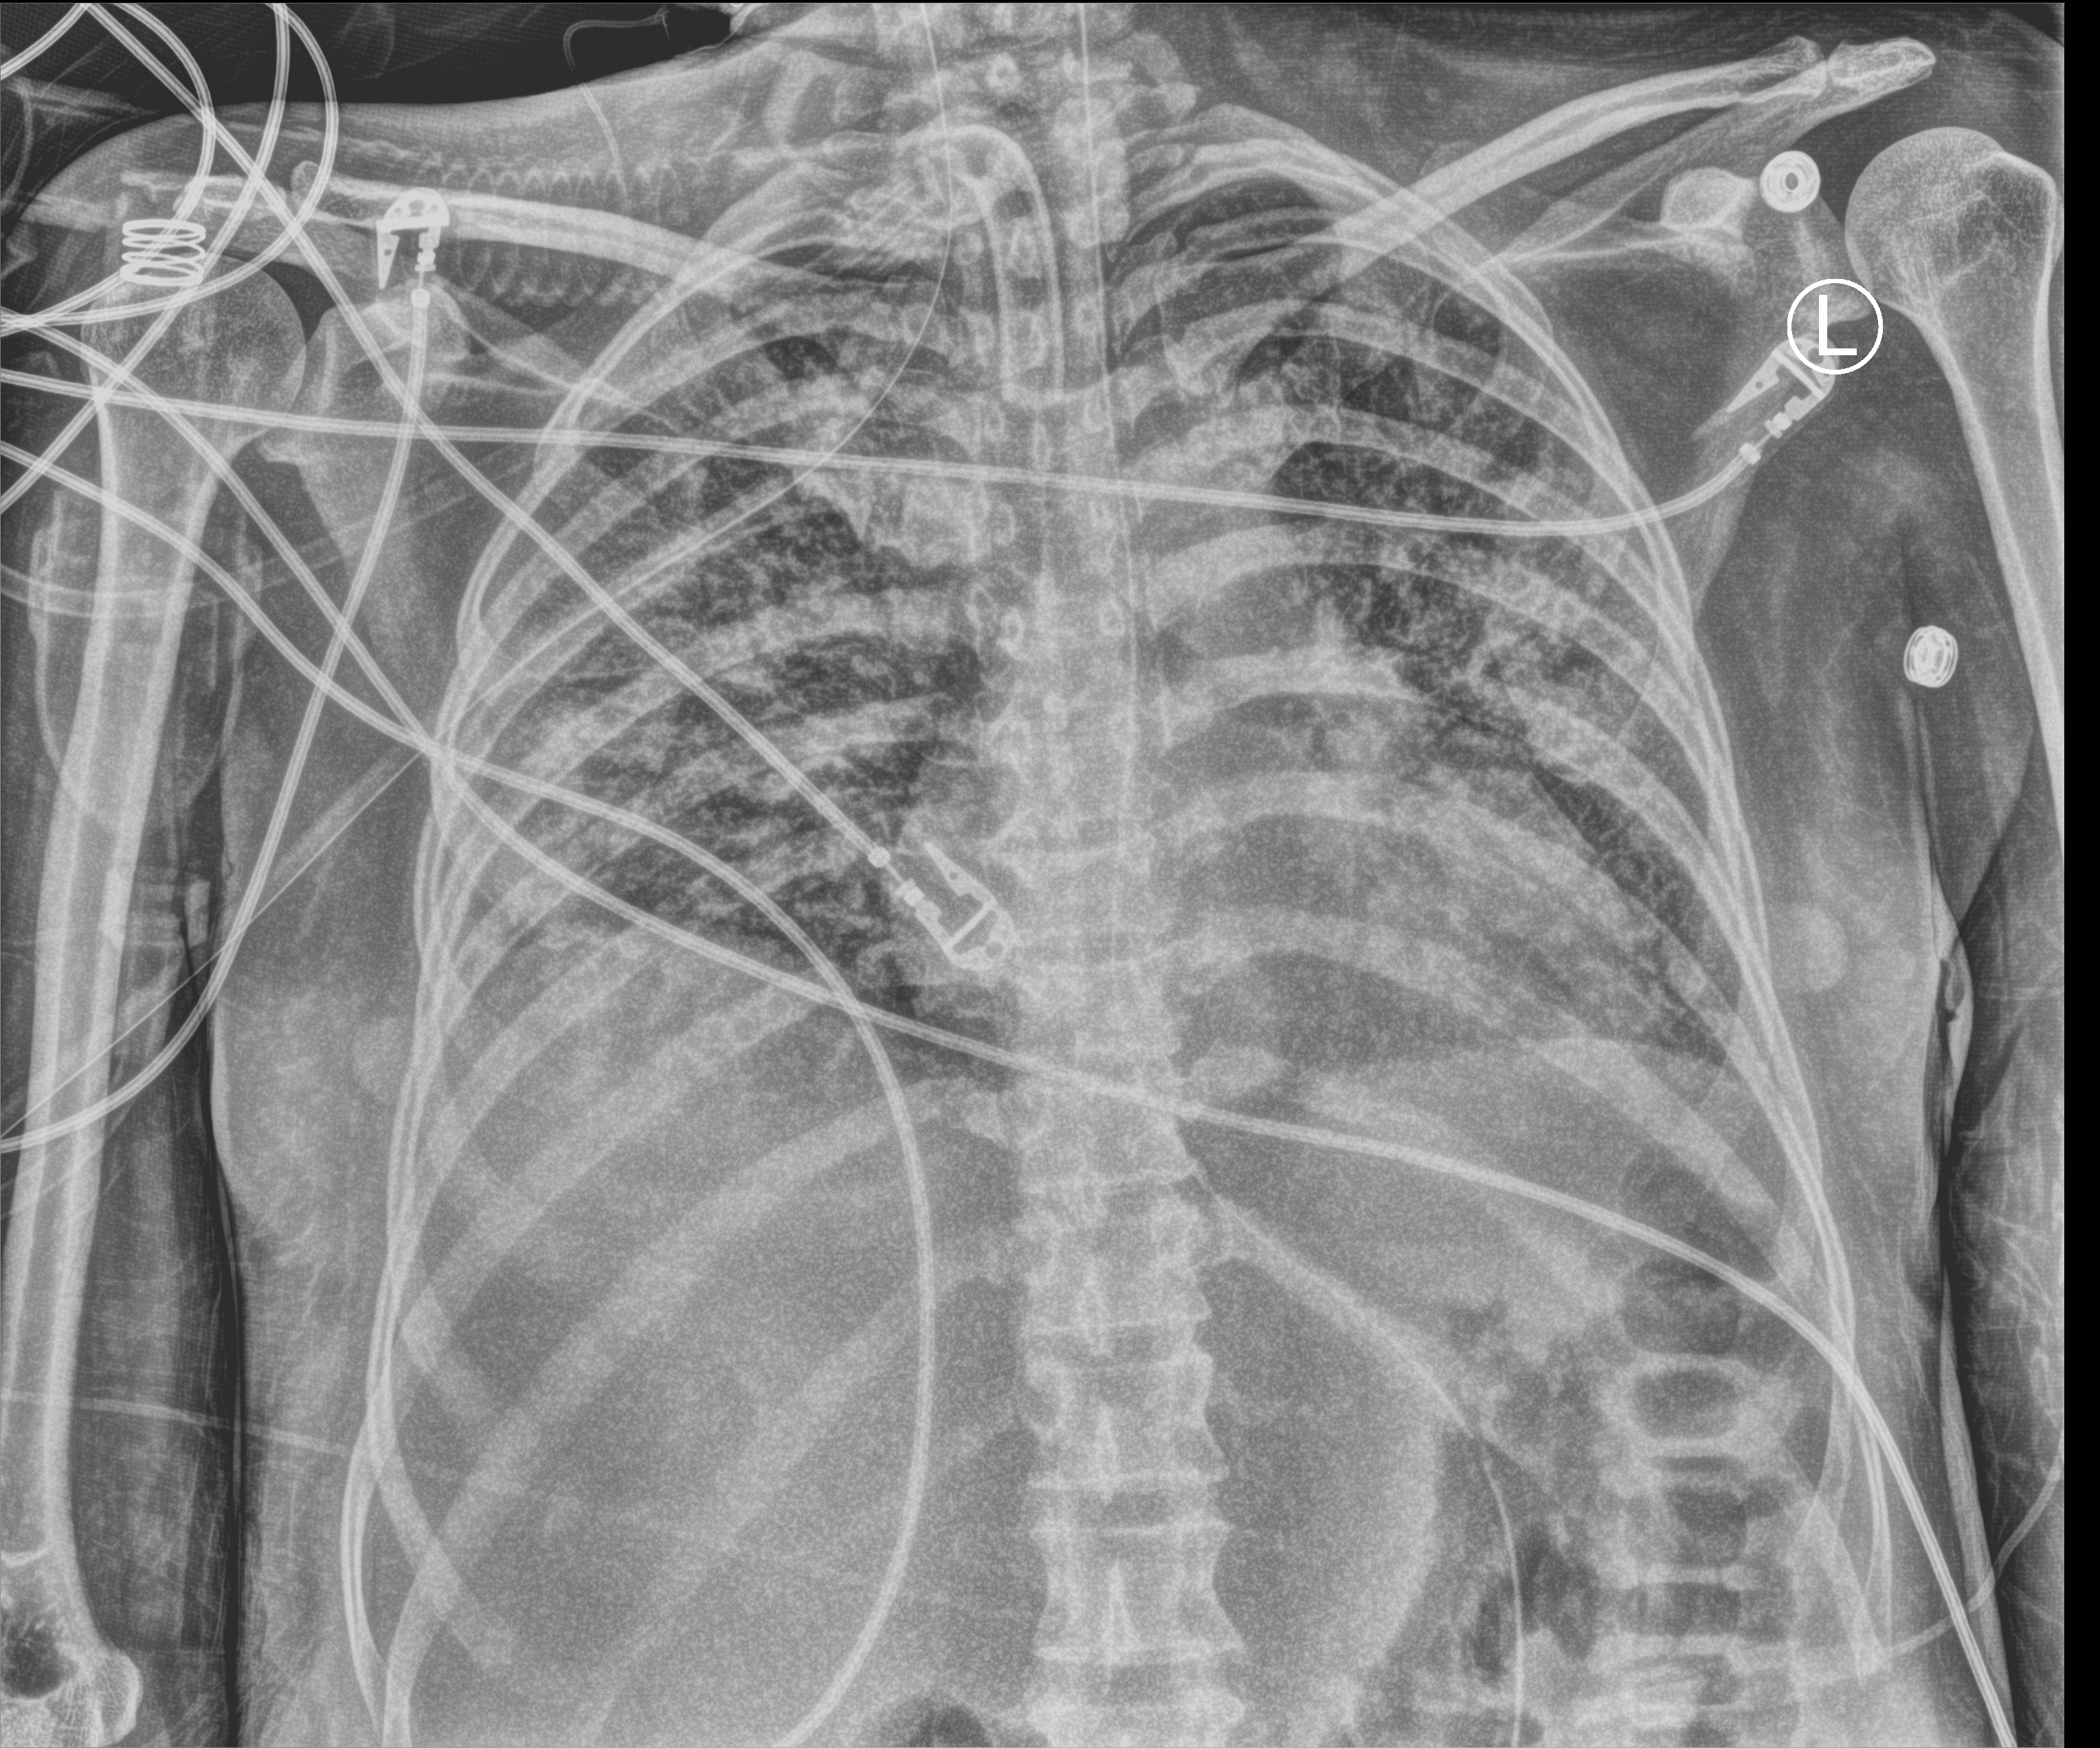
Bedside chest radiograph (computed radiography), anteroposterior (AP) projection. Female patient hospitalised with COVID-19, age 18–59 years.
From the hospital-stay record, not from the radiograph (when in the stay this image was taken is not recorded):
- admitted to intensive care during this hospital stay: yes
- COPD (admission record): no
- mechanically ventilated during this hospital stay: yes